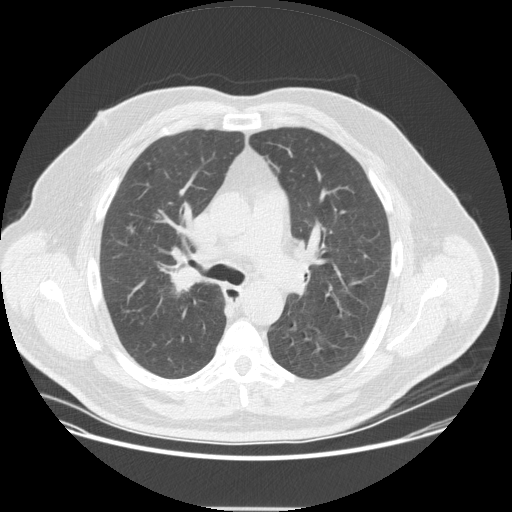
Low-dose screening chest CT, axial slice. Second annual screen. Lung window (W 1500 / L -600 HU). 2.5 mm slice thickness. Slice 125 of 351 in the series. 512 × 512 image matrix, field of view 419 × 419 mm. Male participant, aged 57 years at enrolment.
Expert reader's lesion annotation, box from (x=153, y=254) to (x=211, y=307) px. The exam's reader record, not a measurement of the box and not confirmed to be the same lesion: non-calcified nodule or mass ≥4 mm, right upper lobe, 20 × 16 mm, spiculated (stellate) margins, soft tissue attenuation, pre-existing on the prior screen: no.